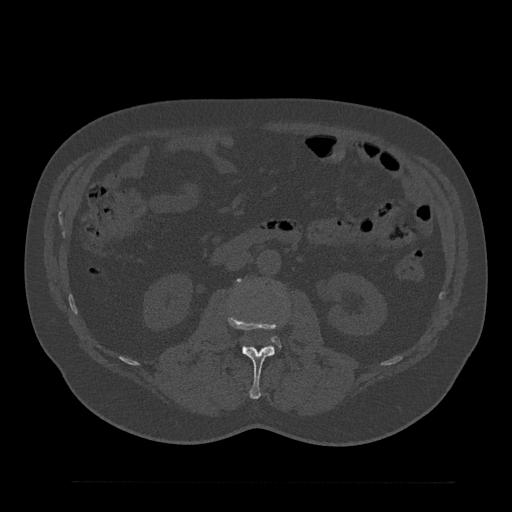
CT including the spine, one axial slice. Slice 78 of 797 in the series (ordered by position). Reconstruction kernel Br40s/3. 120 kVp. Bone window (W 1800 / L 400 HU). 512 × 512 image matrix. Male patient, age 61 years. Case-level facts recorded for this patient, not image findings: primary cancer: prostate.
Annotated regions visible in this slice (semi-automatic segmentation, software-assisted and operator-edited):
- L2 vertebra: bounding box (x1, y1, x2, y2) in pixels: (228, 313, 287, 399)
- L3 vertebra: (272, 337, 279, 345)